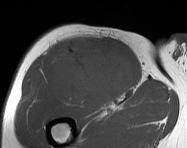
MRI of an extremity soft-tissue mass, one axial slice; position 97 of 114 along the scan axis; MR volume resampled by the dataset authors to the PET/CT grid (not the native acquisition matrix); 3.27 mm slice thickness; 187 × 148 image matrix. Male patient. From the clinical record (not read from this slice): histological type: pleiomorphic leiomyosarcoma; grade: intermediate; site of the primary tumour: right thigh.
Structures marked on this image (expert contour drawn on MRI and transferred to this co-registered scan by the dataset authors):
- gross tumour volume including surrounding oedema: bounding box [x1, y1, x2, y2] px = [50, 36, 135, 108]
- gross tumour volume (mass): [50, 36, 135, 108]